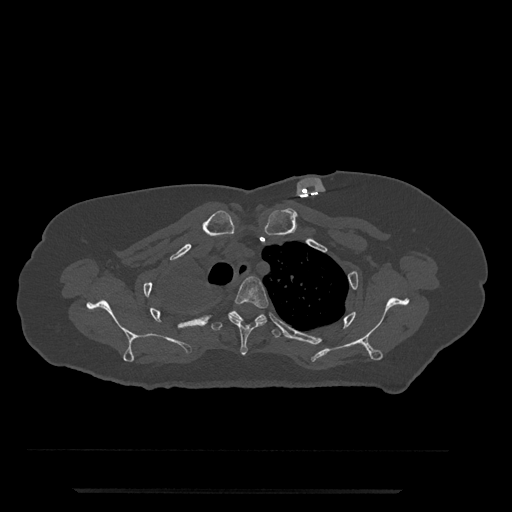
CT including the spine, one axial slice; slice 619 of 797 in the series (ordered by position); reconstruction kernel Br40s/3; bone window (W 1800 / L 400 HU); 0.5 mm slice thickness; 512 × 512 image matrix. Patient: female, 51 years. From the clinical record (not read from this slice): primary cancer: neuro.
Annotated regions visible in this slice (semi-automatic segmentation, software-assisted and operator-edited):
- T3 vertebra: bounding box (x1, y1, x2, y2) in pixels: (228, 276, 269, 355)
- T4 vertebra: (211, 310, 282, 338)